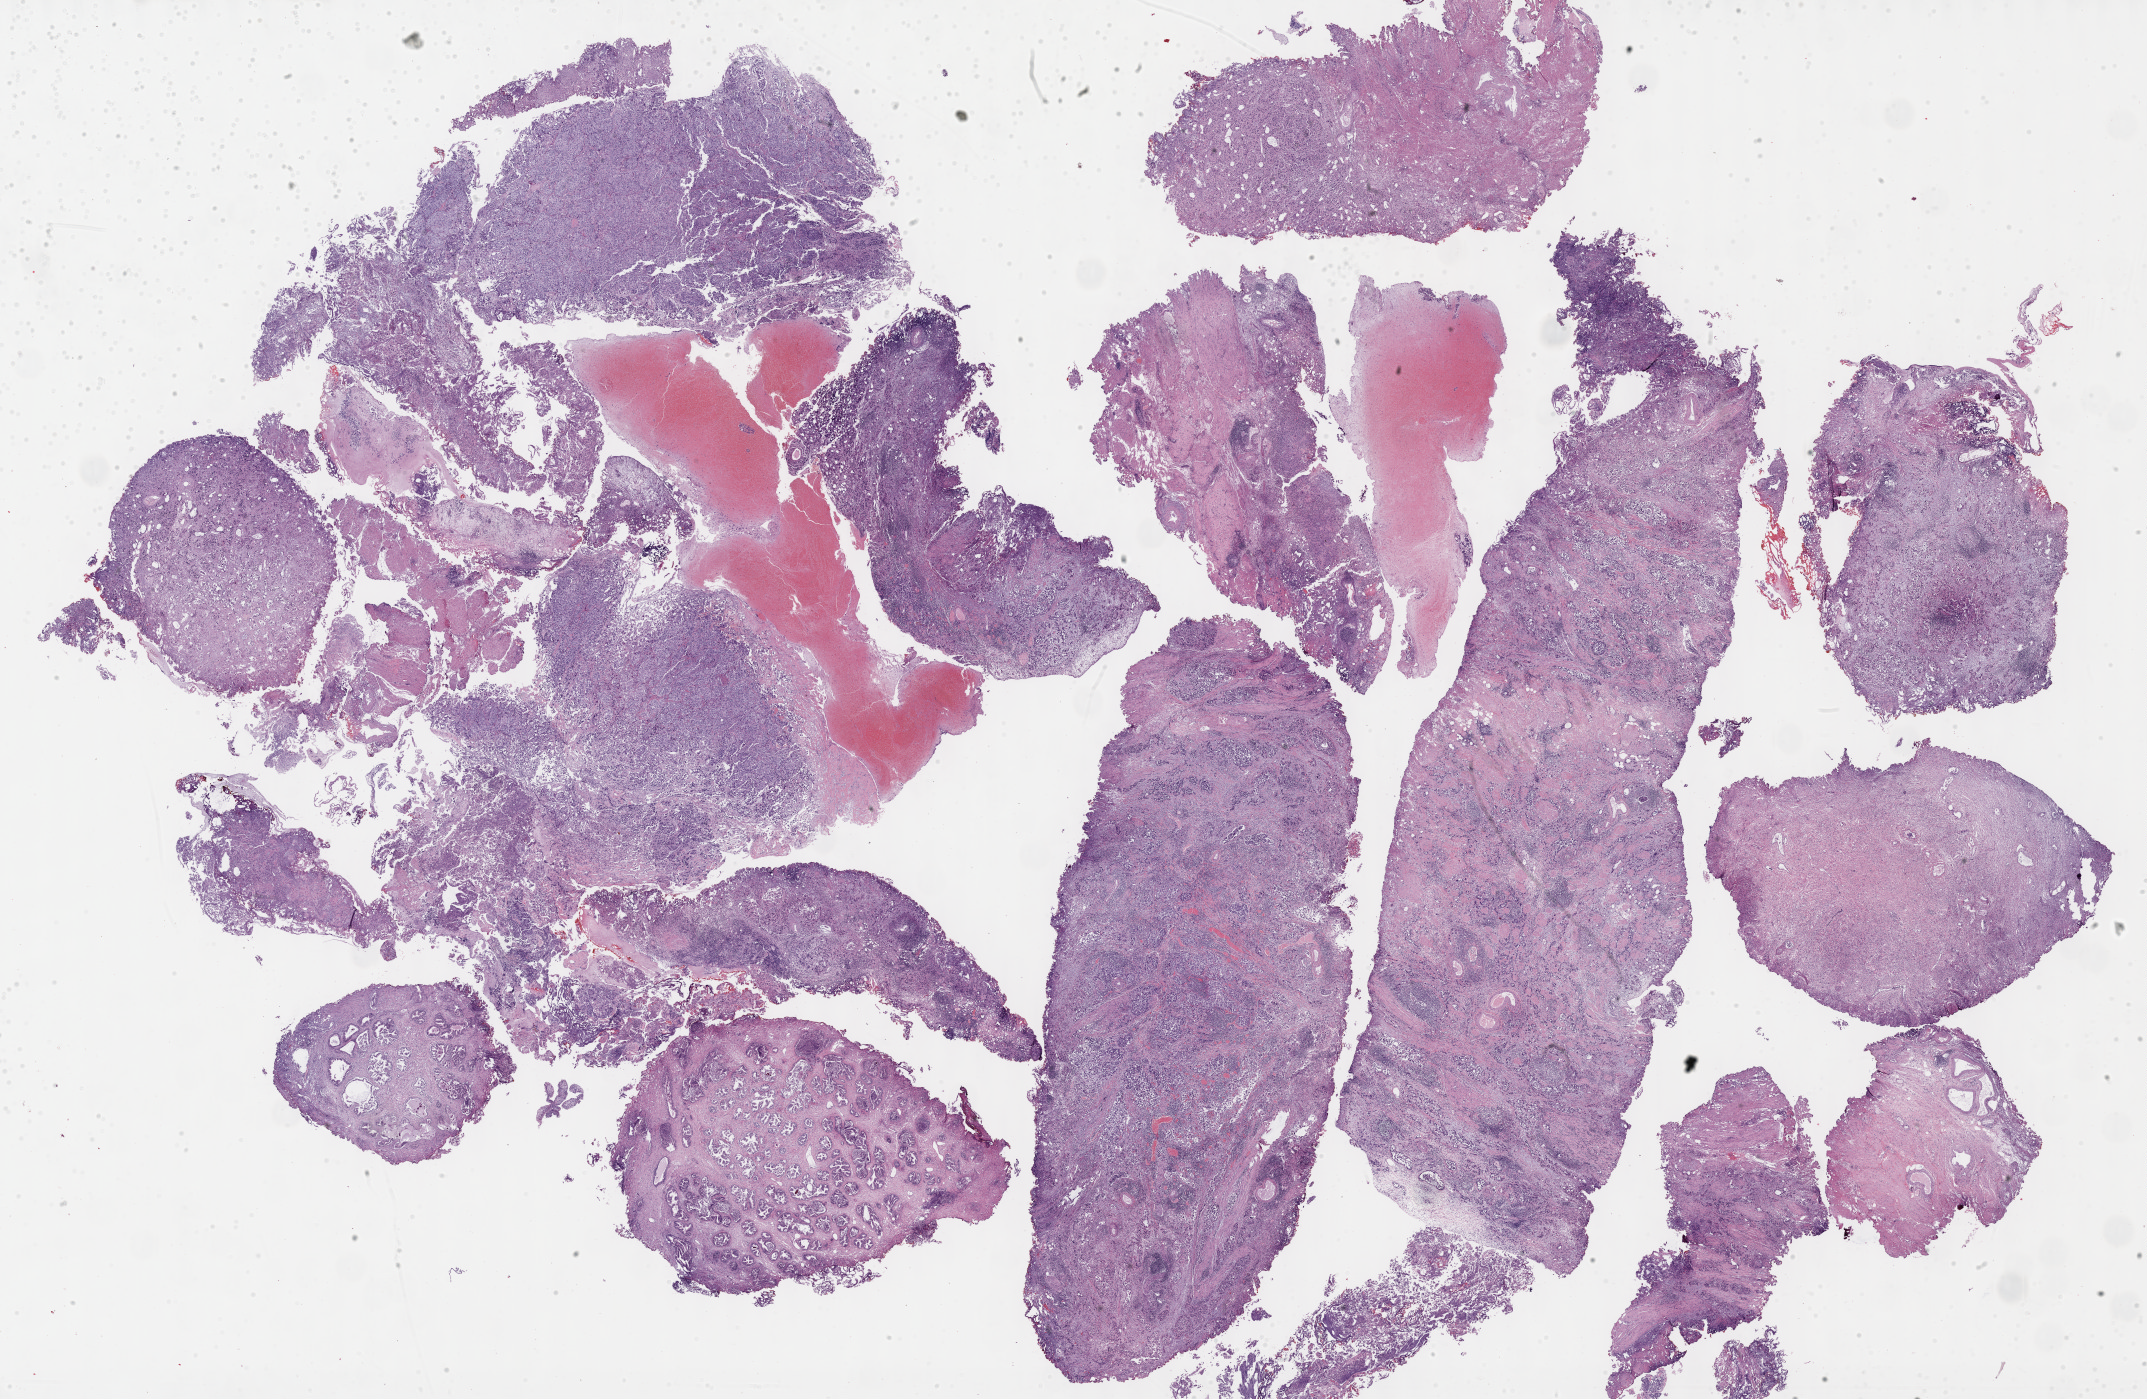
Whole-slide histology image, Hematoxylin and eosin (H&E) stained — shown as a low-resolution overview of the whole scanned area (about 34.7 x 22.6 mm, from a 40x scan), formalin-fixed paraffin-embedded (FFPE) diagnostic section, sample: primary tumour, bladder. Male, age 77 years at initial diagnosis. Histologic grade: high grade.
Diagnosis: Transitional cell carcinoma. TNM: T3 N1 M0. AJCC pathologic stage: IV (7th edition).